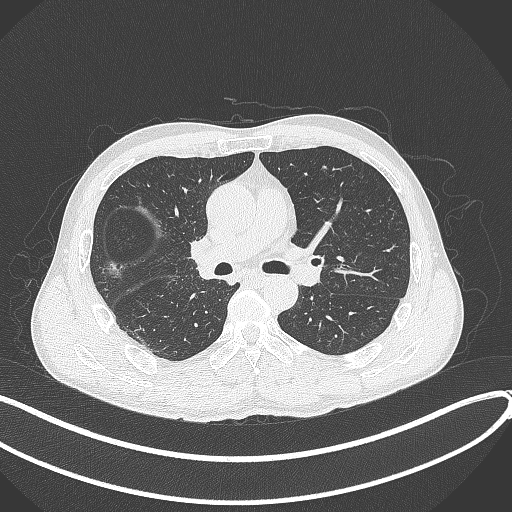
Chest CT, one axial slice. Slice 227 of 409 in the series (ordered by position). 120 kVp. Lung window (W 1500 / L -600 HU). 1 mm slice thickness. 512 × 512 image matrix, field of view 400 × 400 mm. Male patient, age 53 years. Case-level facts recorded for this patient, not image findings: clinical TNM (as recorded): T1b N0 M0.
Outlined on this slice (rectangle marked by the reading radiologist):
- lung tumour (recorded histology: squamous cell carcinoma): bounding box (x1, y1, x2, y2) in pixels: (189, 233, 227, 289)